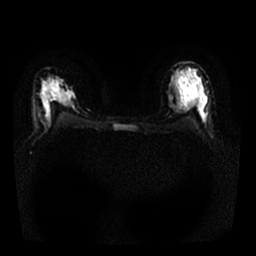
Breast MRI, one axial slice. Slice 15 of 25 in the series (ordered by position). Diffusion-weighted series; image 2 of 4 stored at this slice position (different b-values; order by instance number). 1.5 T. 4 mm slice thickness. 256 × 256 image matrix, field of view 320 × 320 mm. Female patient.
Annotated regions visible in this slice (expert manual segmentation):
- tumour on diffusion-weighted imaging: bounding box (x1, y1, x2, y2) in pixels: (43, 92, 51, 99)